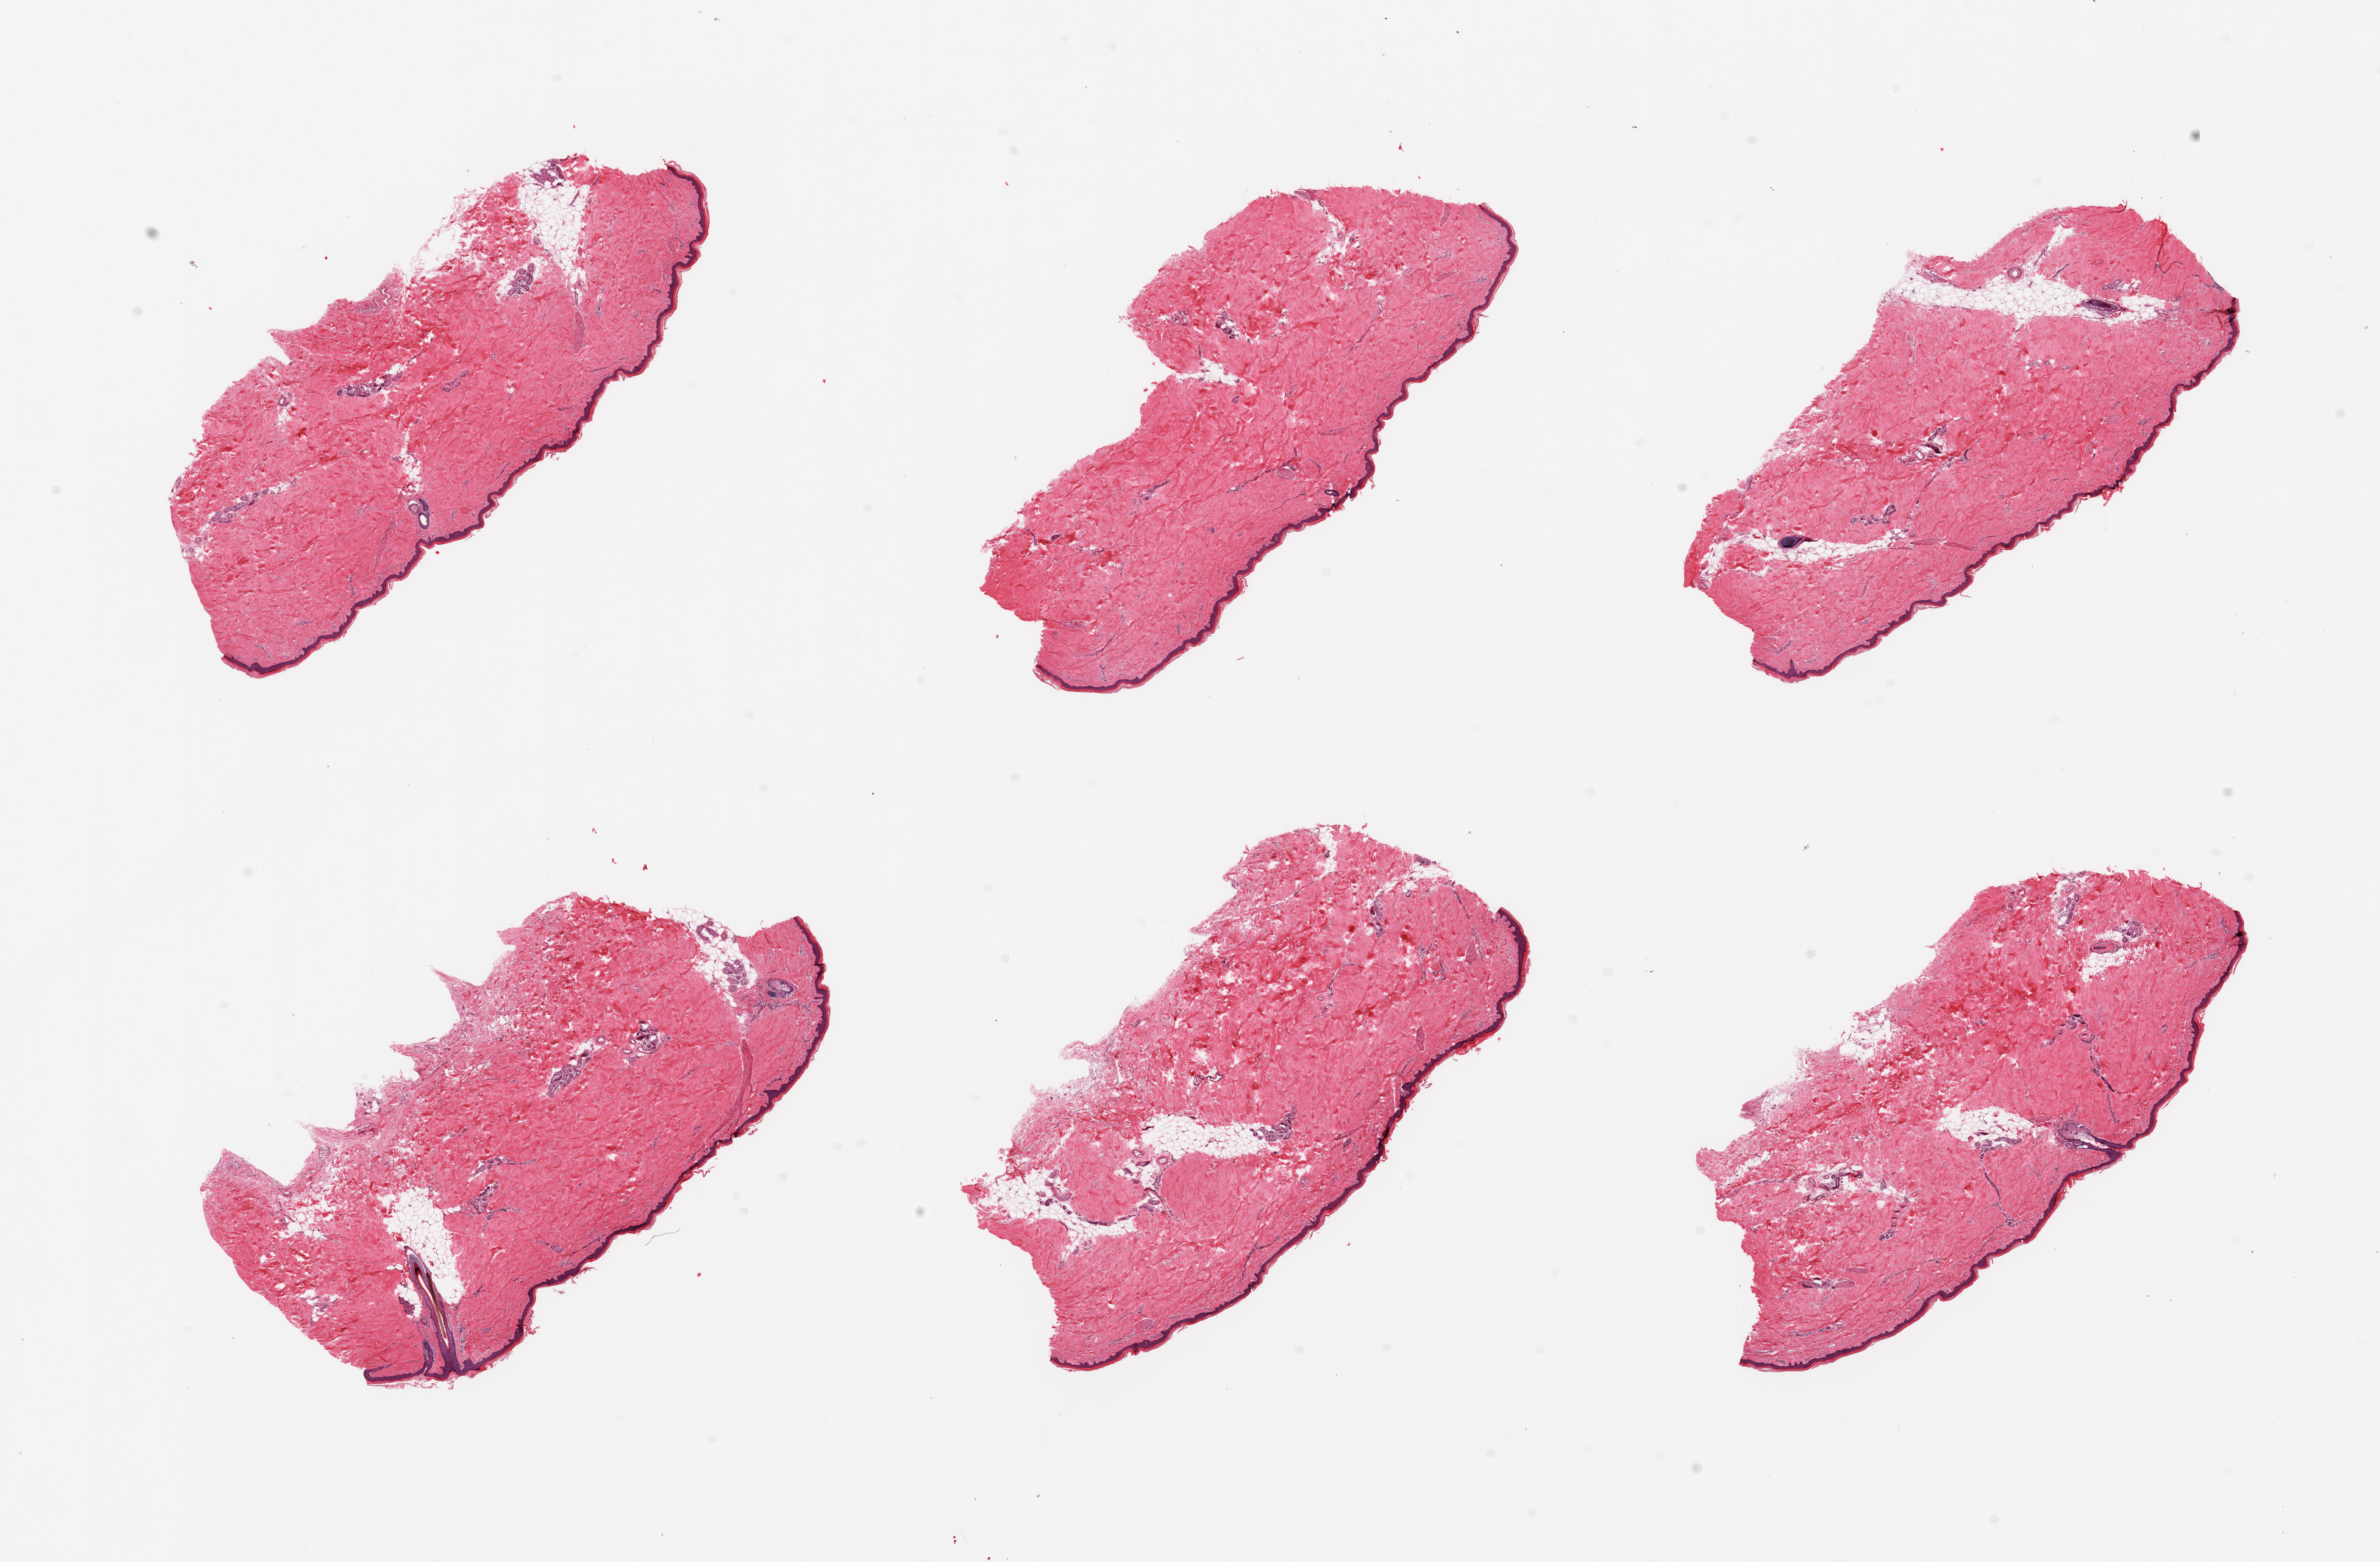
Hematoxylin and eosin (H&E) whole-slide image — a low-resolution overview of the entire scanned area, about 25.6 x 16.8 mm (slide scanned at 20x); PAXgene-fixed paraffin-embedded (PFPE) section; target tissue: skin of lower leg; donor tissue sample.
- review note (as recorded): 6 pieces, no adherent dermal fat; squamous epithelium is ~45-50 microns